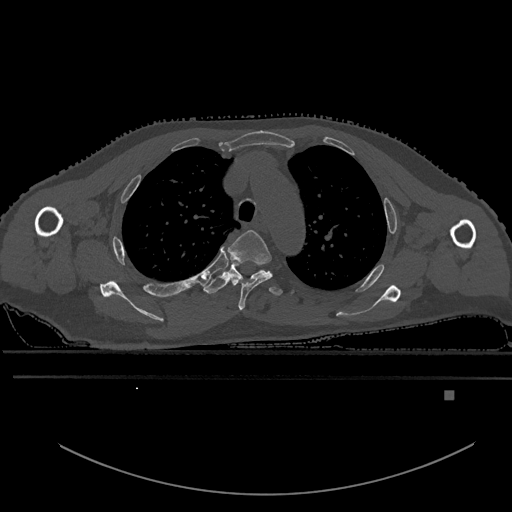
CT including the spine, one axial slice. Position 431 of 969 along the scan axis. Bone window (W 1800 / L 400 HU). 0.5 mm slice thickness. 512 × 512 image matrix. Male patient, age 82 years. Case-level facts recorded for this patient, not image findings: primary cancer: prostate; vertebrae with lytic lesions (as recorded): T11, T9, T8, T2.
Annotated regions visible in this slice (semi-automatic segmentation, software-assisted and operator-edited):
- T3 vertebra: box from (x=228, y=230) to (x=272, y=311) px
- T4 vertebra: (x=203, y=262)–(x=283, y=296)